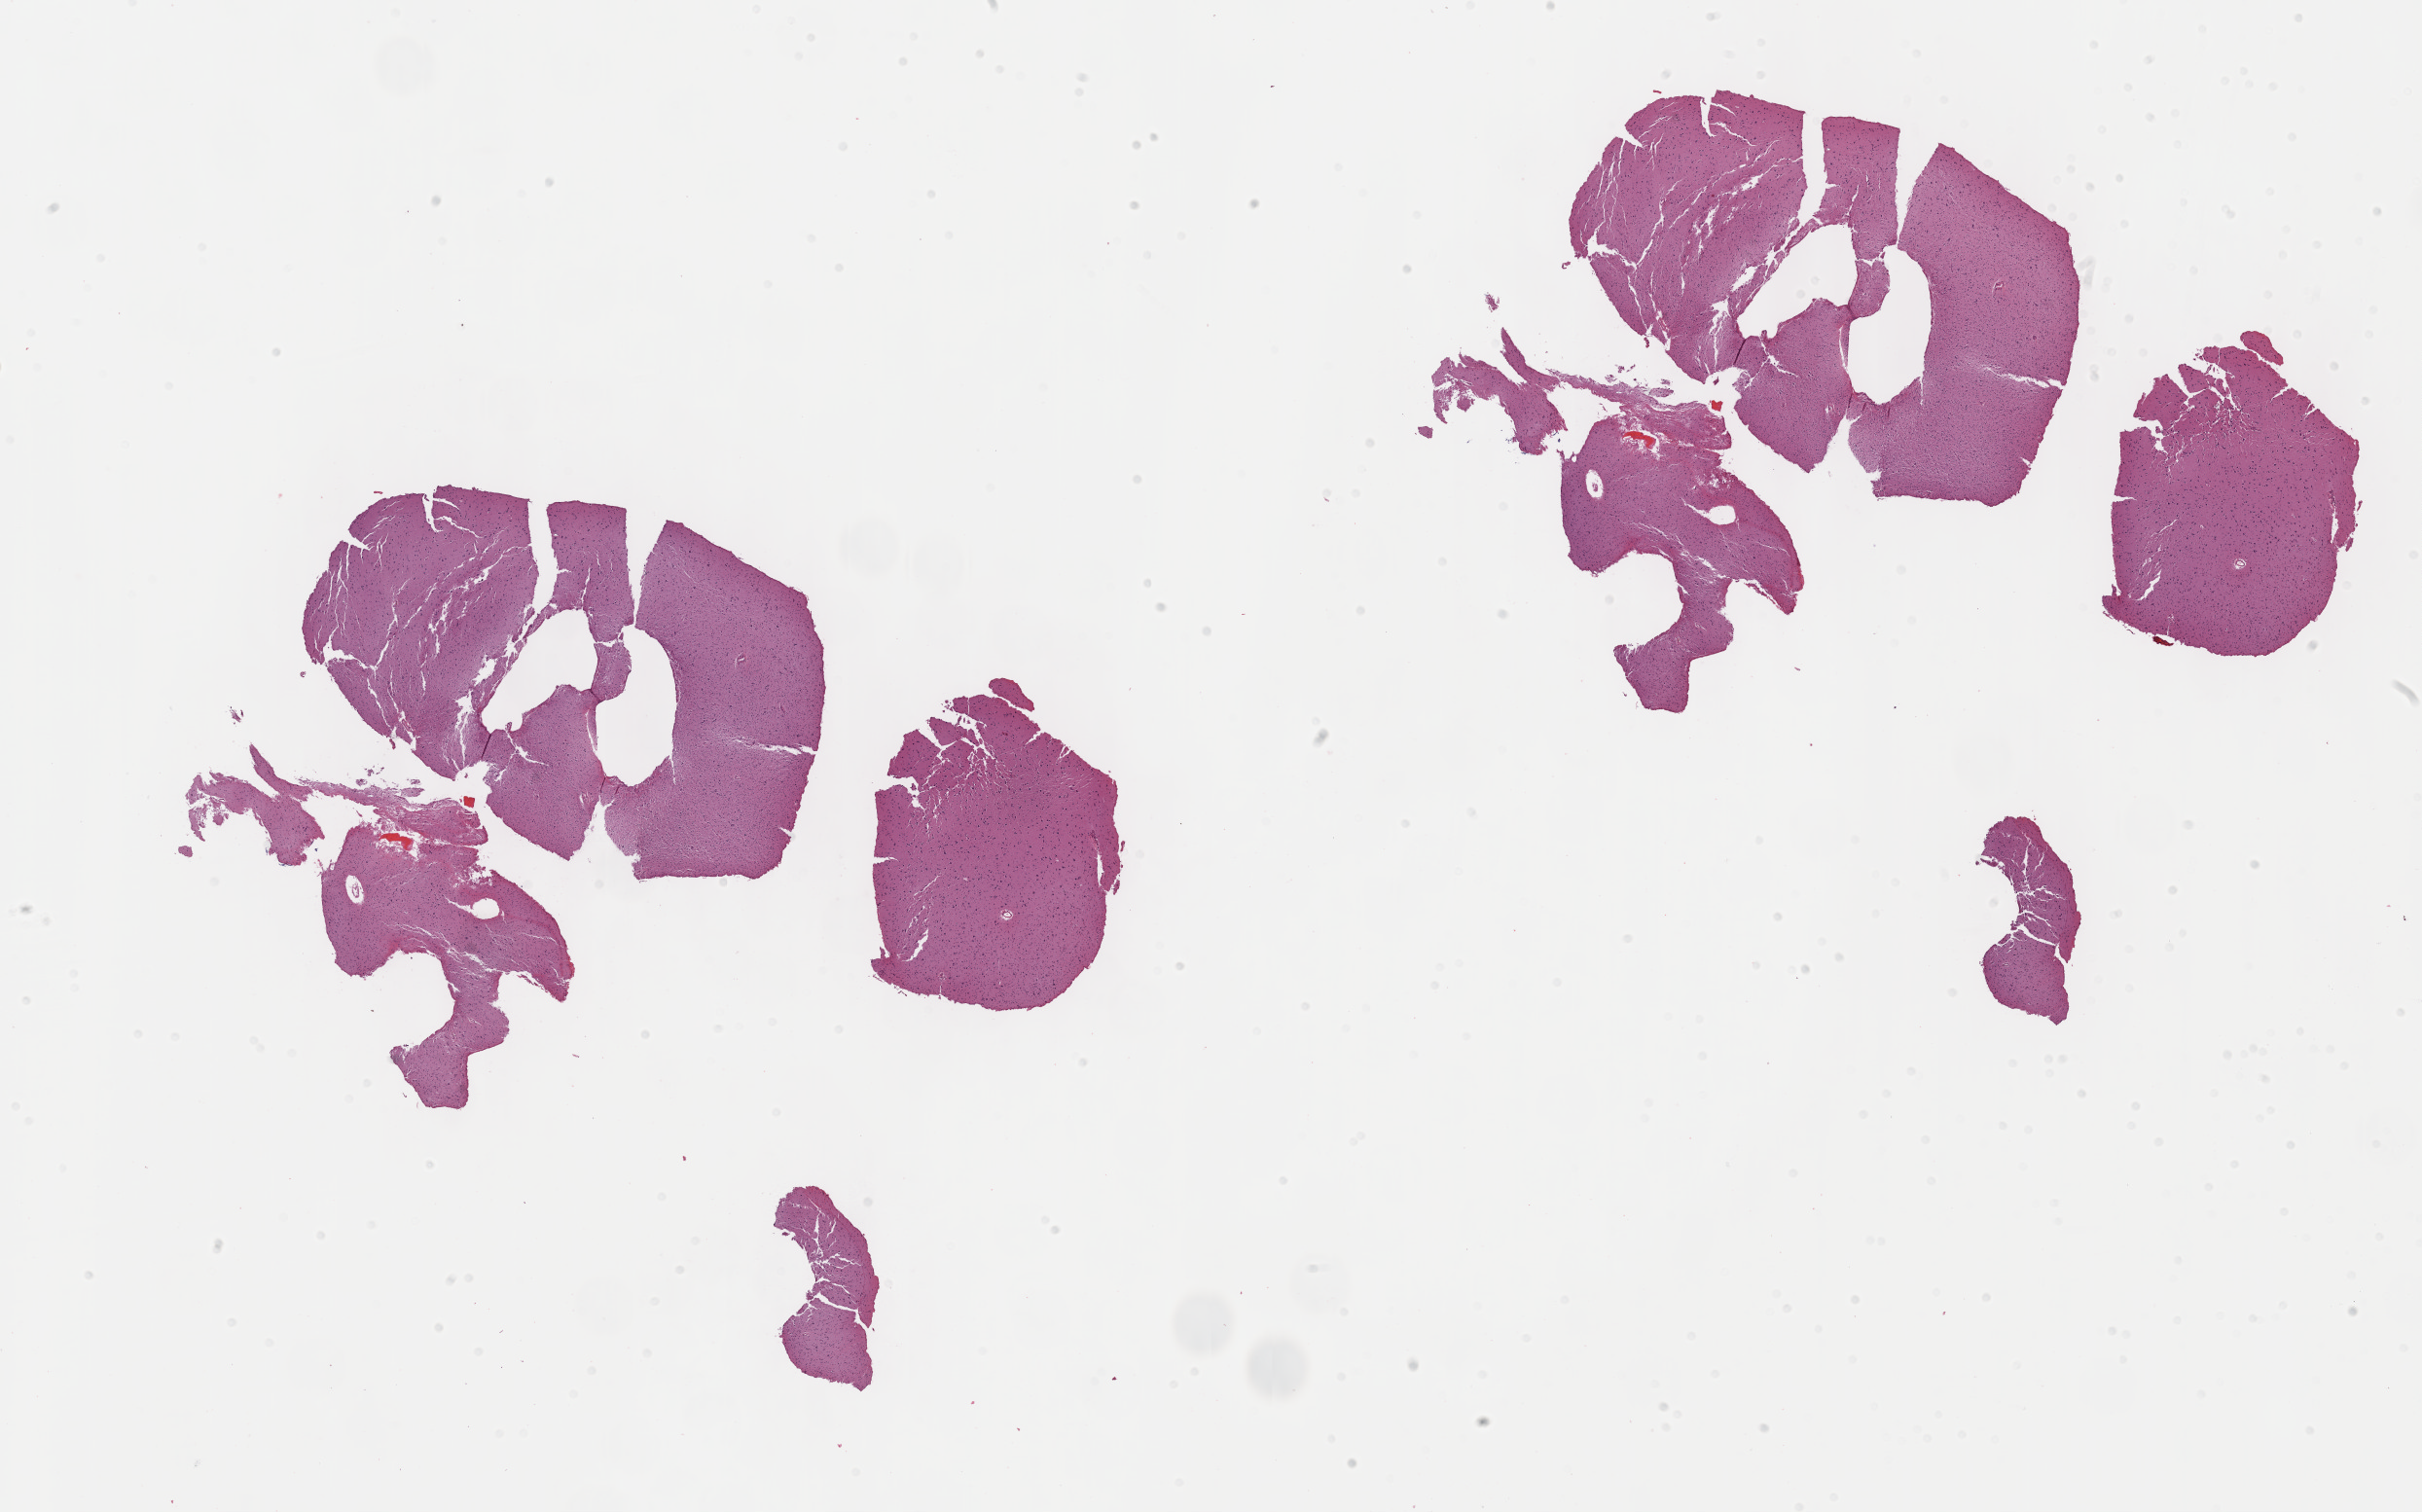
Whole-slide histology image, Hematoxylin and eosin (H&E) stained — shown as a low-resolution overview of the whole scanned area (about 20.1 x 12.6 mm), formalin-fixed paraffin-embedded (FFPE) diagnostic section, brain, primary tumour sample. Male, age 21 years at initial diagnosis. Histologic grade: G2 (moderately differentiated).
Histologic diagnosis: Oligodendroglioma, NOS.